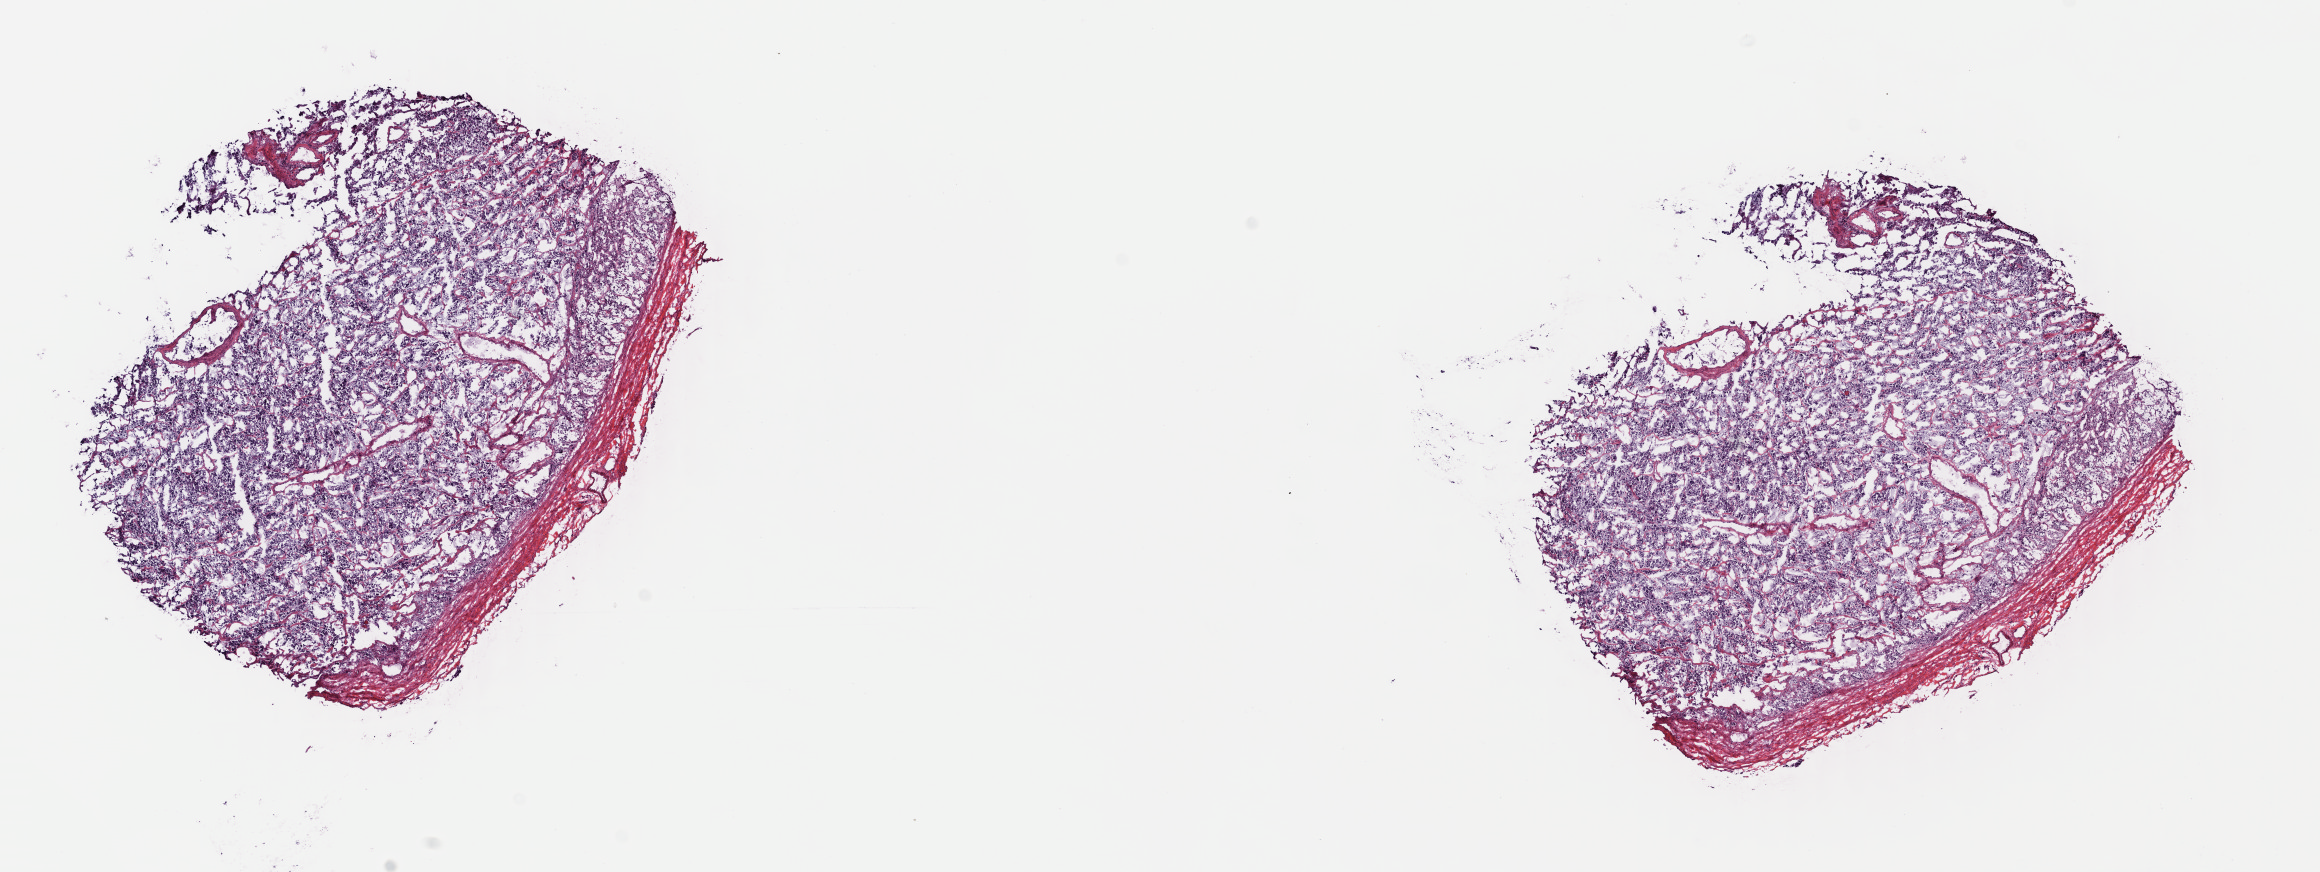
Digitized Hematoxylin and eosin (H&E) stained tissue section (whole slide) — shown as a low-resolution overview of the whole scanned area (about 18.2 x 6.9 mm, slide scanned at 40x), frozen section from the top of the tissue portion, sample: primary tumour, adrenal gland. Female, age 46 years at initial diagnosis. Slide review estimates, as recorded: tumour cells 80%, tumour nuclei 80%.
Pathologic diagnosis: Pheochromocytoma, NOS.